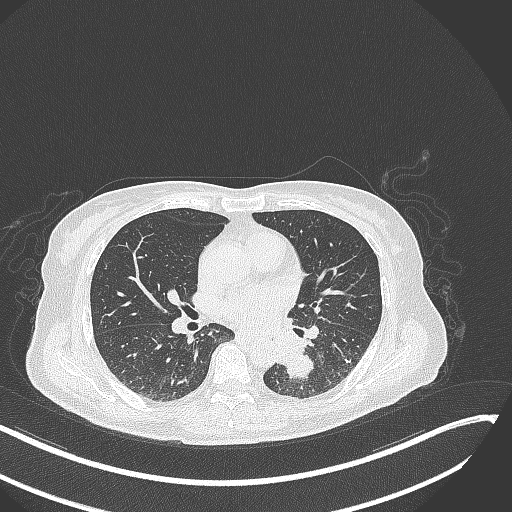
Chest CT, one axial slice. Slice 134 of 342 in the series (ordered by position). Reconstruction kernel B70f. 120 kVp. Lung window (W 1500 / L -600 HU). 512 × 512 image matrix. Patient: female, 64 years. Case-level facts recorded for this patient, not image findings: clinical TNM (as recorded): T3 N1 M1.
Annotated regions visible in this slice (bounding box drawn by a radiologist):
- lung tumour (recorded histology: small cell carcinoma): bounding box <273,324,322,384> (left, top, right, bottom; pixels)